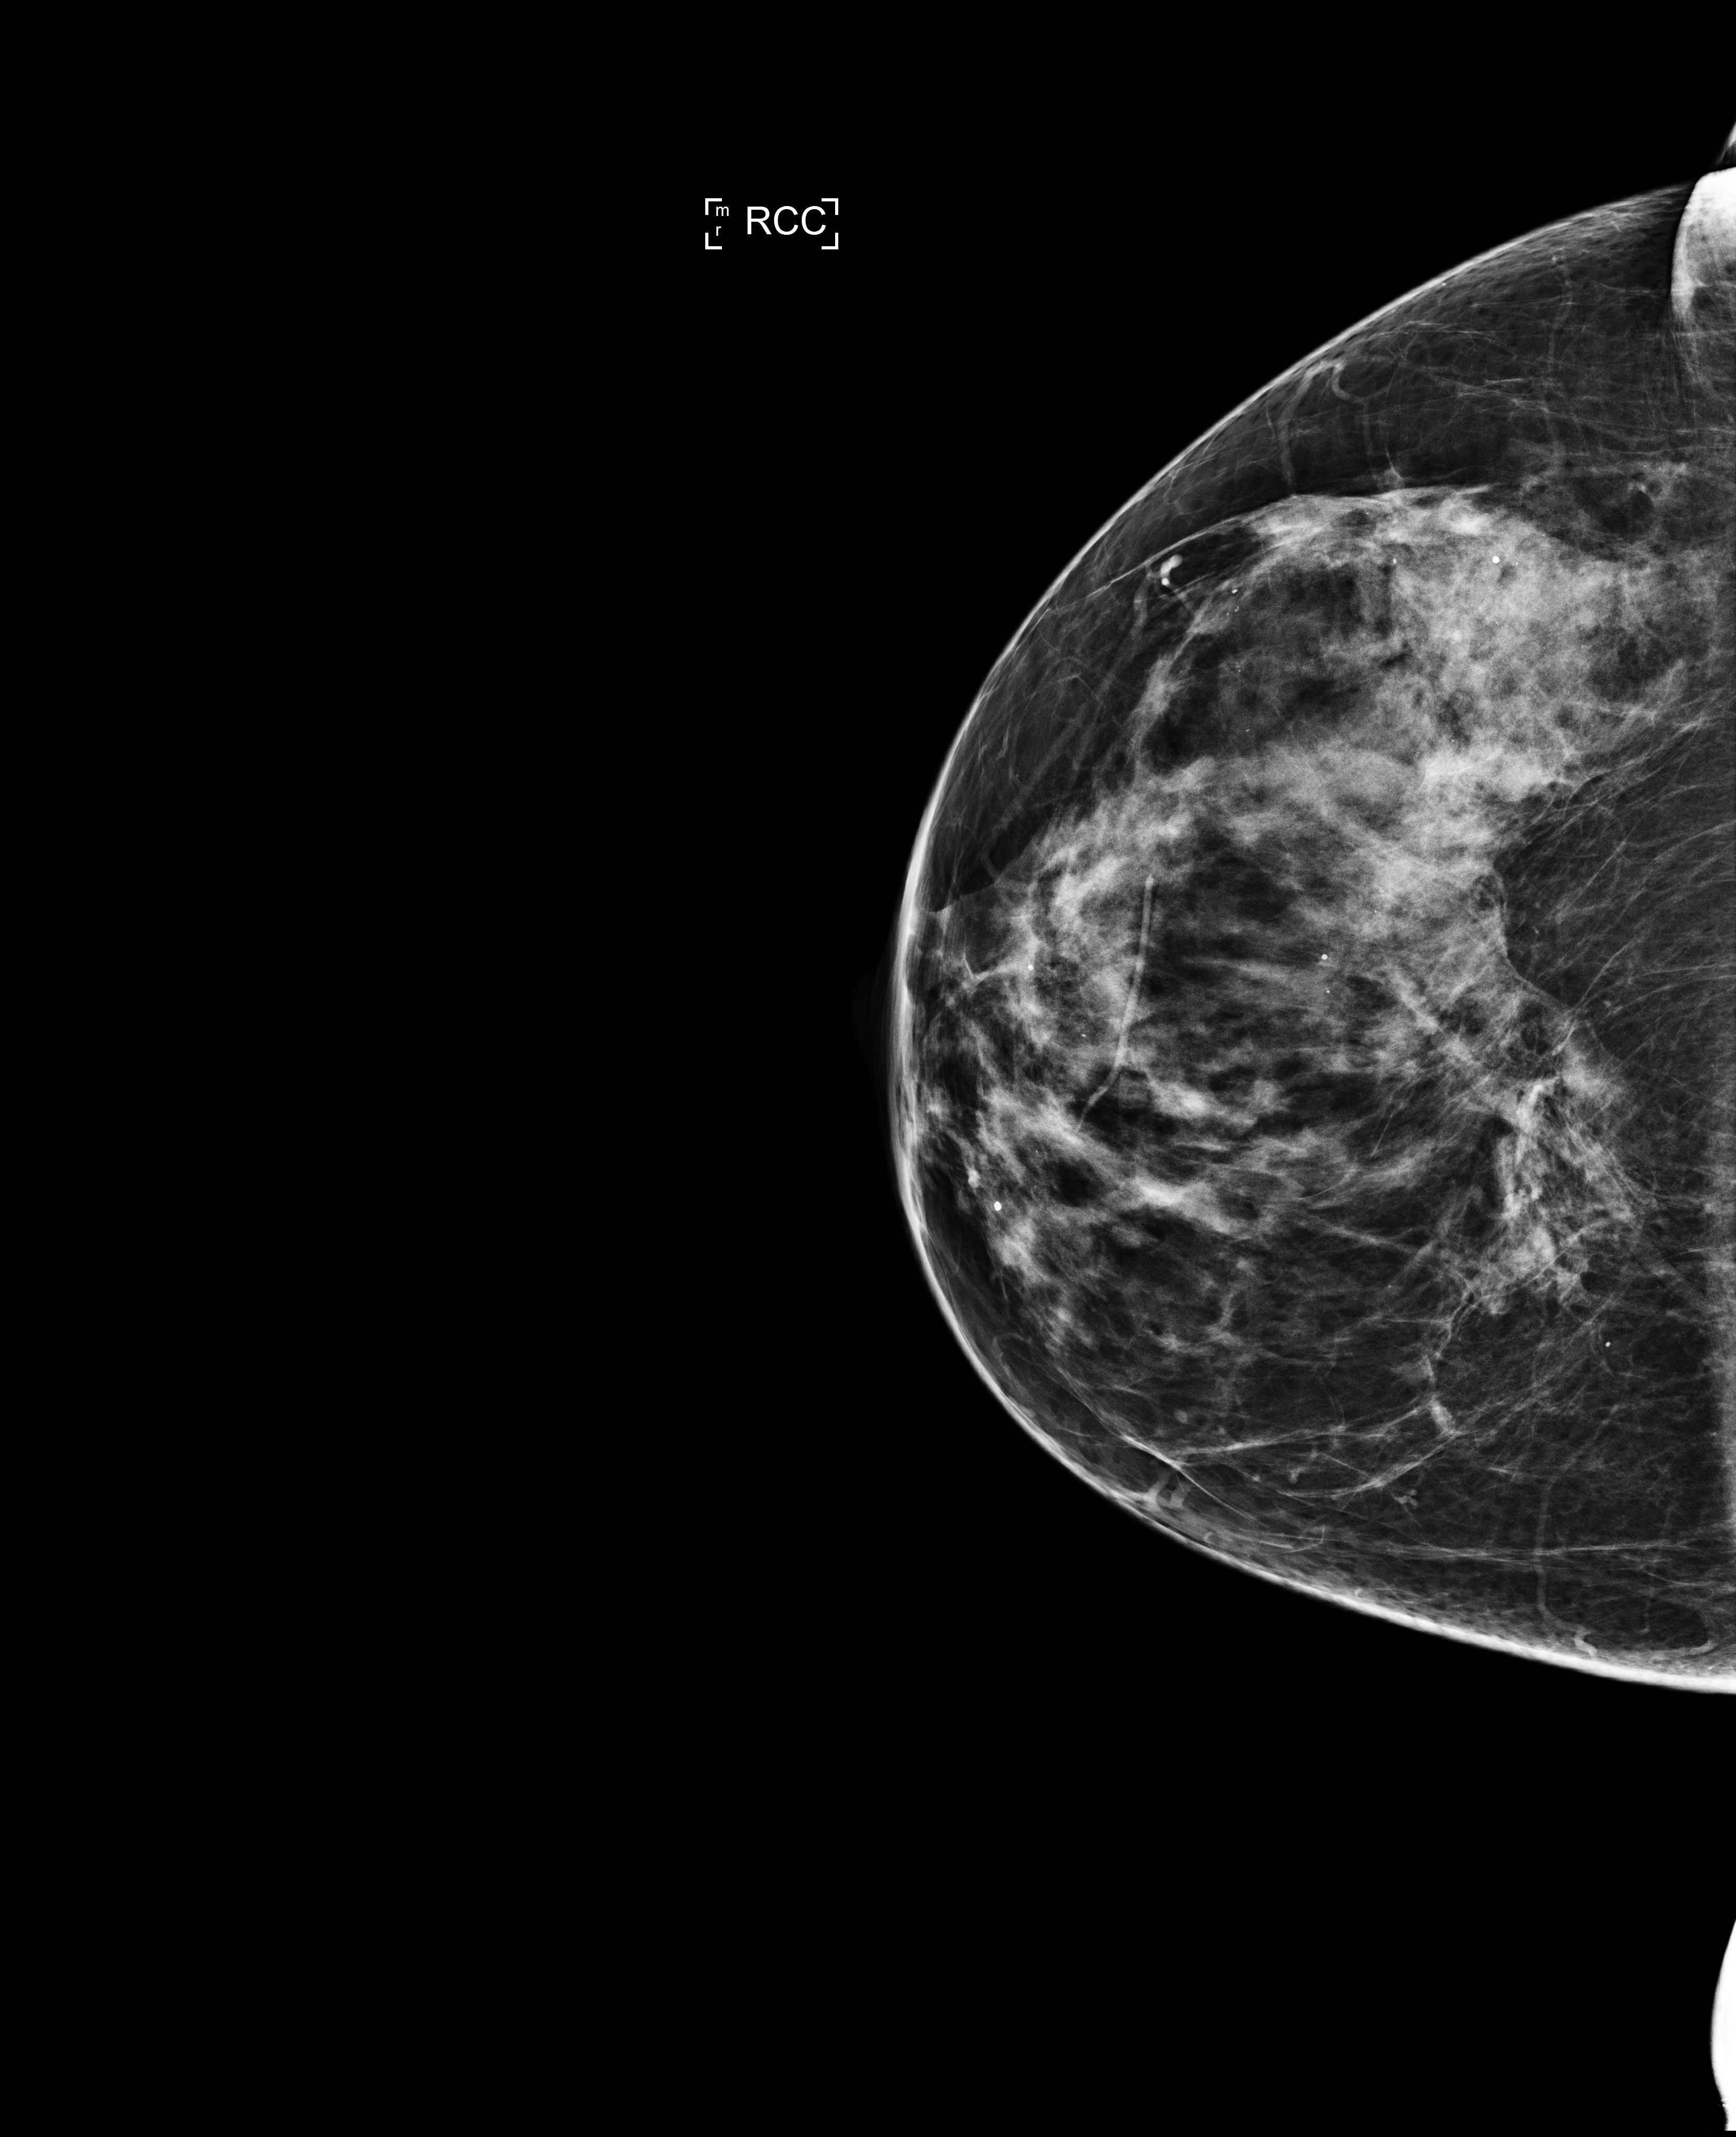
Digital mammogram (FFDM); right breast; CC view; screening examination; compressed breast thickness 68 mm; system: Selenia Dimensions. Female patient, age 59 years.
Breast density at the screening exam (both breasts): heterogeneously dense (BI-RADS density category c). Final BI-RADS assessment for this screening round (tomosynthesis exam, both breasts): category 2. Recall: no recall after this screen.